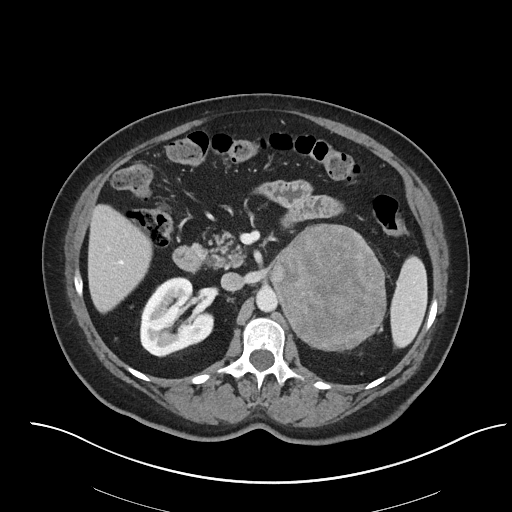
Contrast-enhanced abdominal CT, one axial slice; slice 41 of 92 in the series (ordered by position); 120 kVp; intravenous contrast given; soft-tissue window (W 400 / L 40 HU); 3 mm slice thickness; 512 × 512 image matrix. Patient: female, 53 years. Case-level facts recorded for this patient, not image findings: diagnosis: adrenocortical carcinoma; tumour side: left adrenal.
Structures marked on this image (semi-automatic segmentation, software-assisted and operator-edited):
- mass: box from (x=271, y=224) to (x=385, y=349) px